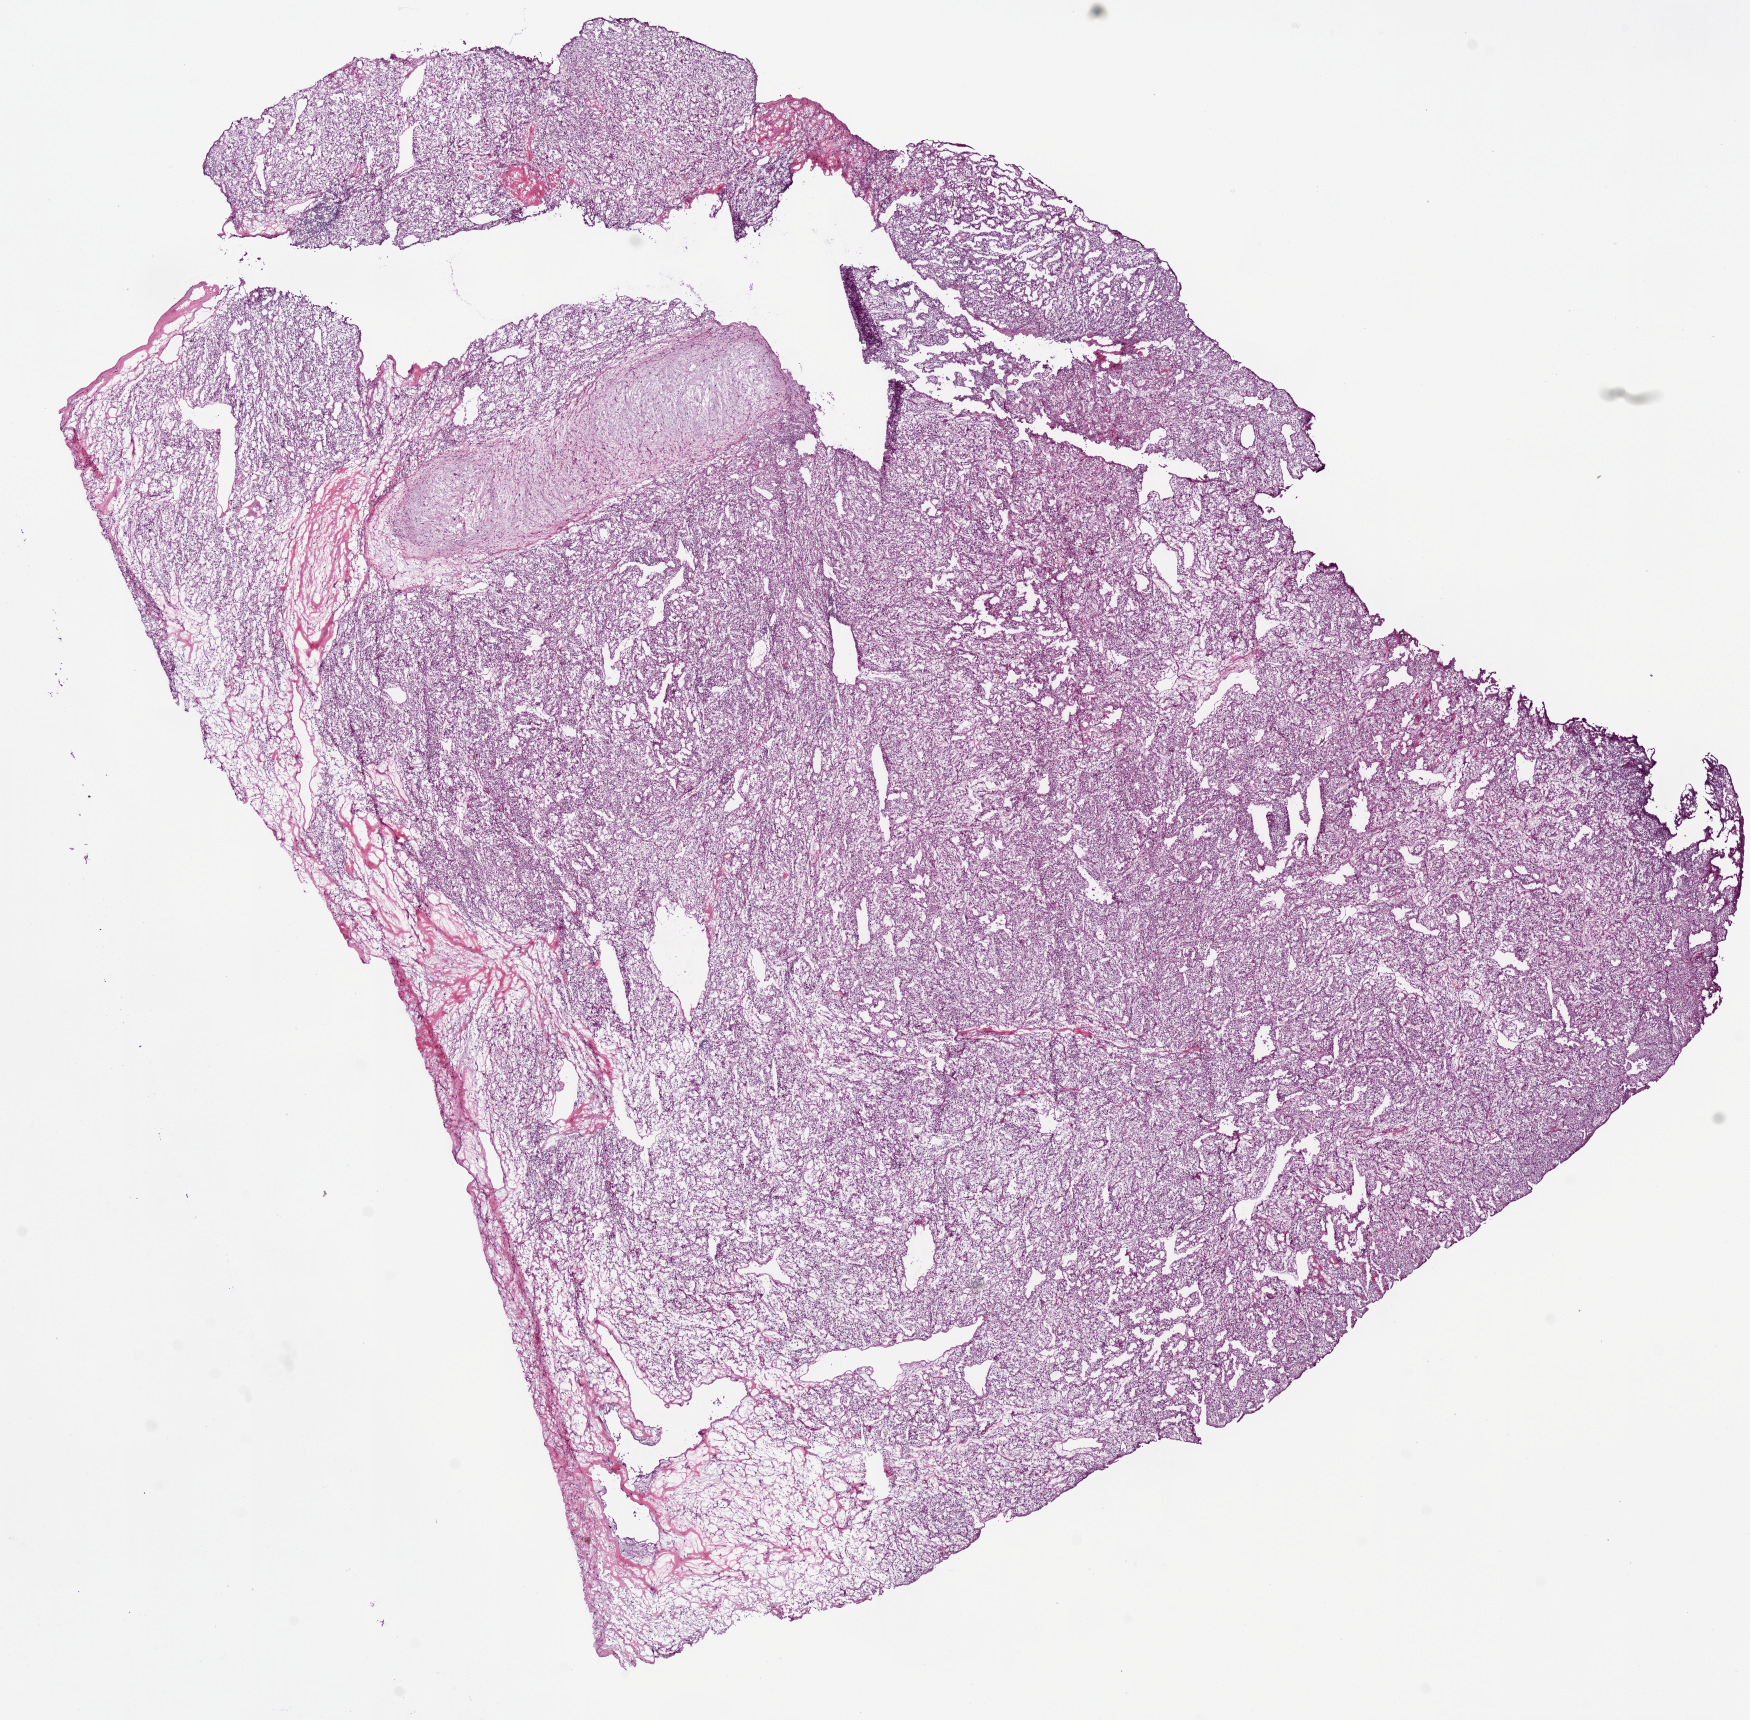
Digitized H&E tissue section (whole slide) — low-resolution overview of the scanned area, about 14.0 x 13.8 mm (slide scanned at 20x), frozen section from the bottom of the tissue portion, sample: primary tumour, kidney. Male, age 52 years at initial diagnosis. Histologic grade: G4 (undifferentiated). Pathologist review of this section (percent, as recorded): tumour cells 85%, tumour nuclei 85%, normal cells 0%, stromal cells 15%, necrosis 0%.
Diagnosis: Clear cell adenocarcinoma, NOS. AJCC pathologic stage: IV. Laterality: right.